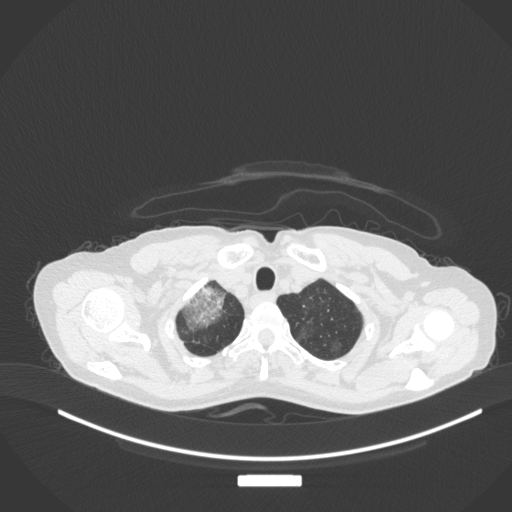
Chest CT, one axial slice. Position 296 of 311 along the scan axis. 120 kVp. Lung window (W 1500 / L -600 HU). 1 mm slice thickness. 512 × 512 image matrix. Patient: female, 59 years. Case-level facts recorded for this patient, not image findings: clinical TNM (as recorded): T3 N0 M0.
Structures marked on this image (rectangle marked by the reading radiologist):
- lung tumour (recorded histology: adenocarcinoma): bounding box [x1, y1, x2, y2] px = [180, 284, 233, 333]